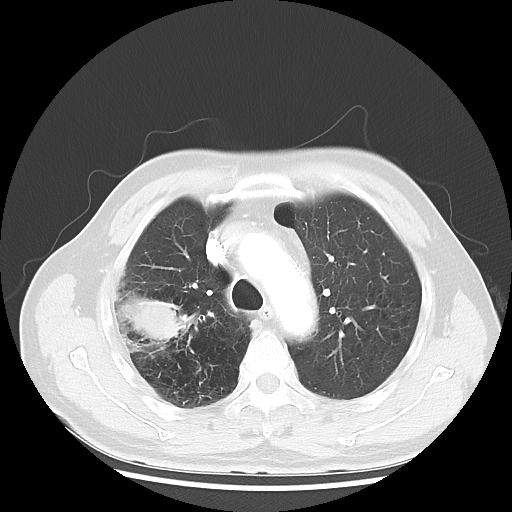
Chest CT, one axial slice; position 37 of 50 along the scan axis; lung window (W 1500 / L -600 HU); 5 mm slice thickness; 512 × 512 image matrix, field of view 360 × 360 mm. Patient: male, 69 years. From the clinical record (not read from this slice): clinical TNM (as recorded): T3 N0 M0; histopathological grade: G3.
Outlined on this slice (rectangle marked by the reading radiologist):
- lung tumour (recorded histology: adenocarcinoma): bounding box [x1, y1, x2, y2] px = [115, 283, 200, 353]